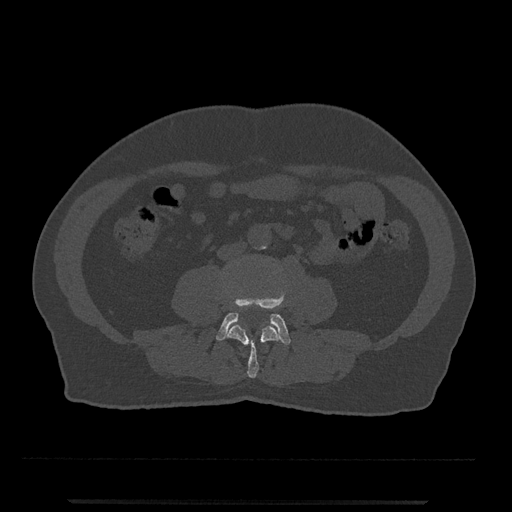
CT including the spine, one axial slice; slice 169 of 797 in the series (ordered by position); bone window (W 1800 / L 400 HU); 0.5 mm slice thickness; 512 × 512 image matrix. Patient: male, 63 years. From the clinical record (not read from this slice): primary cancer: prostate.
Annotated regions visible in this slice (semi-automatic segmentation, software-assisted and operator-edited):
- L3 vertebra: box from (x=227, y=306) to (x=281, y=378) px
- L4 vertebra: (x=216, y=293)–(x=291, y=345)